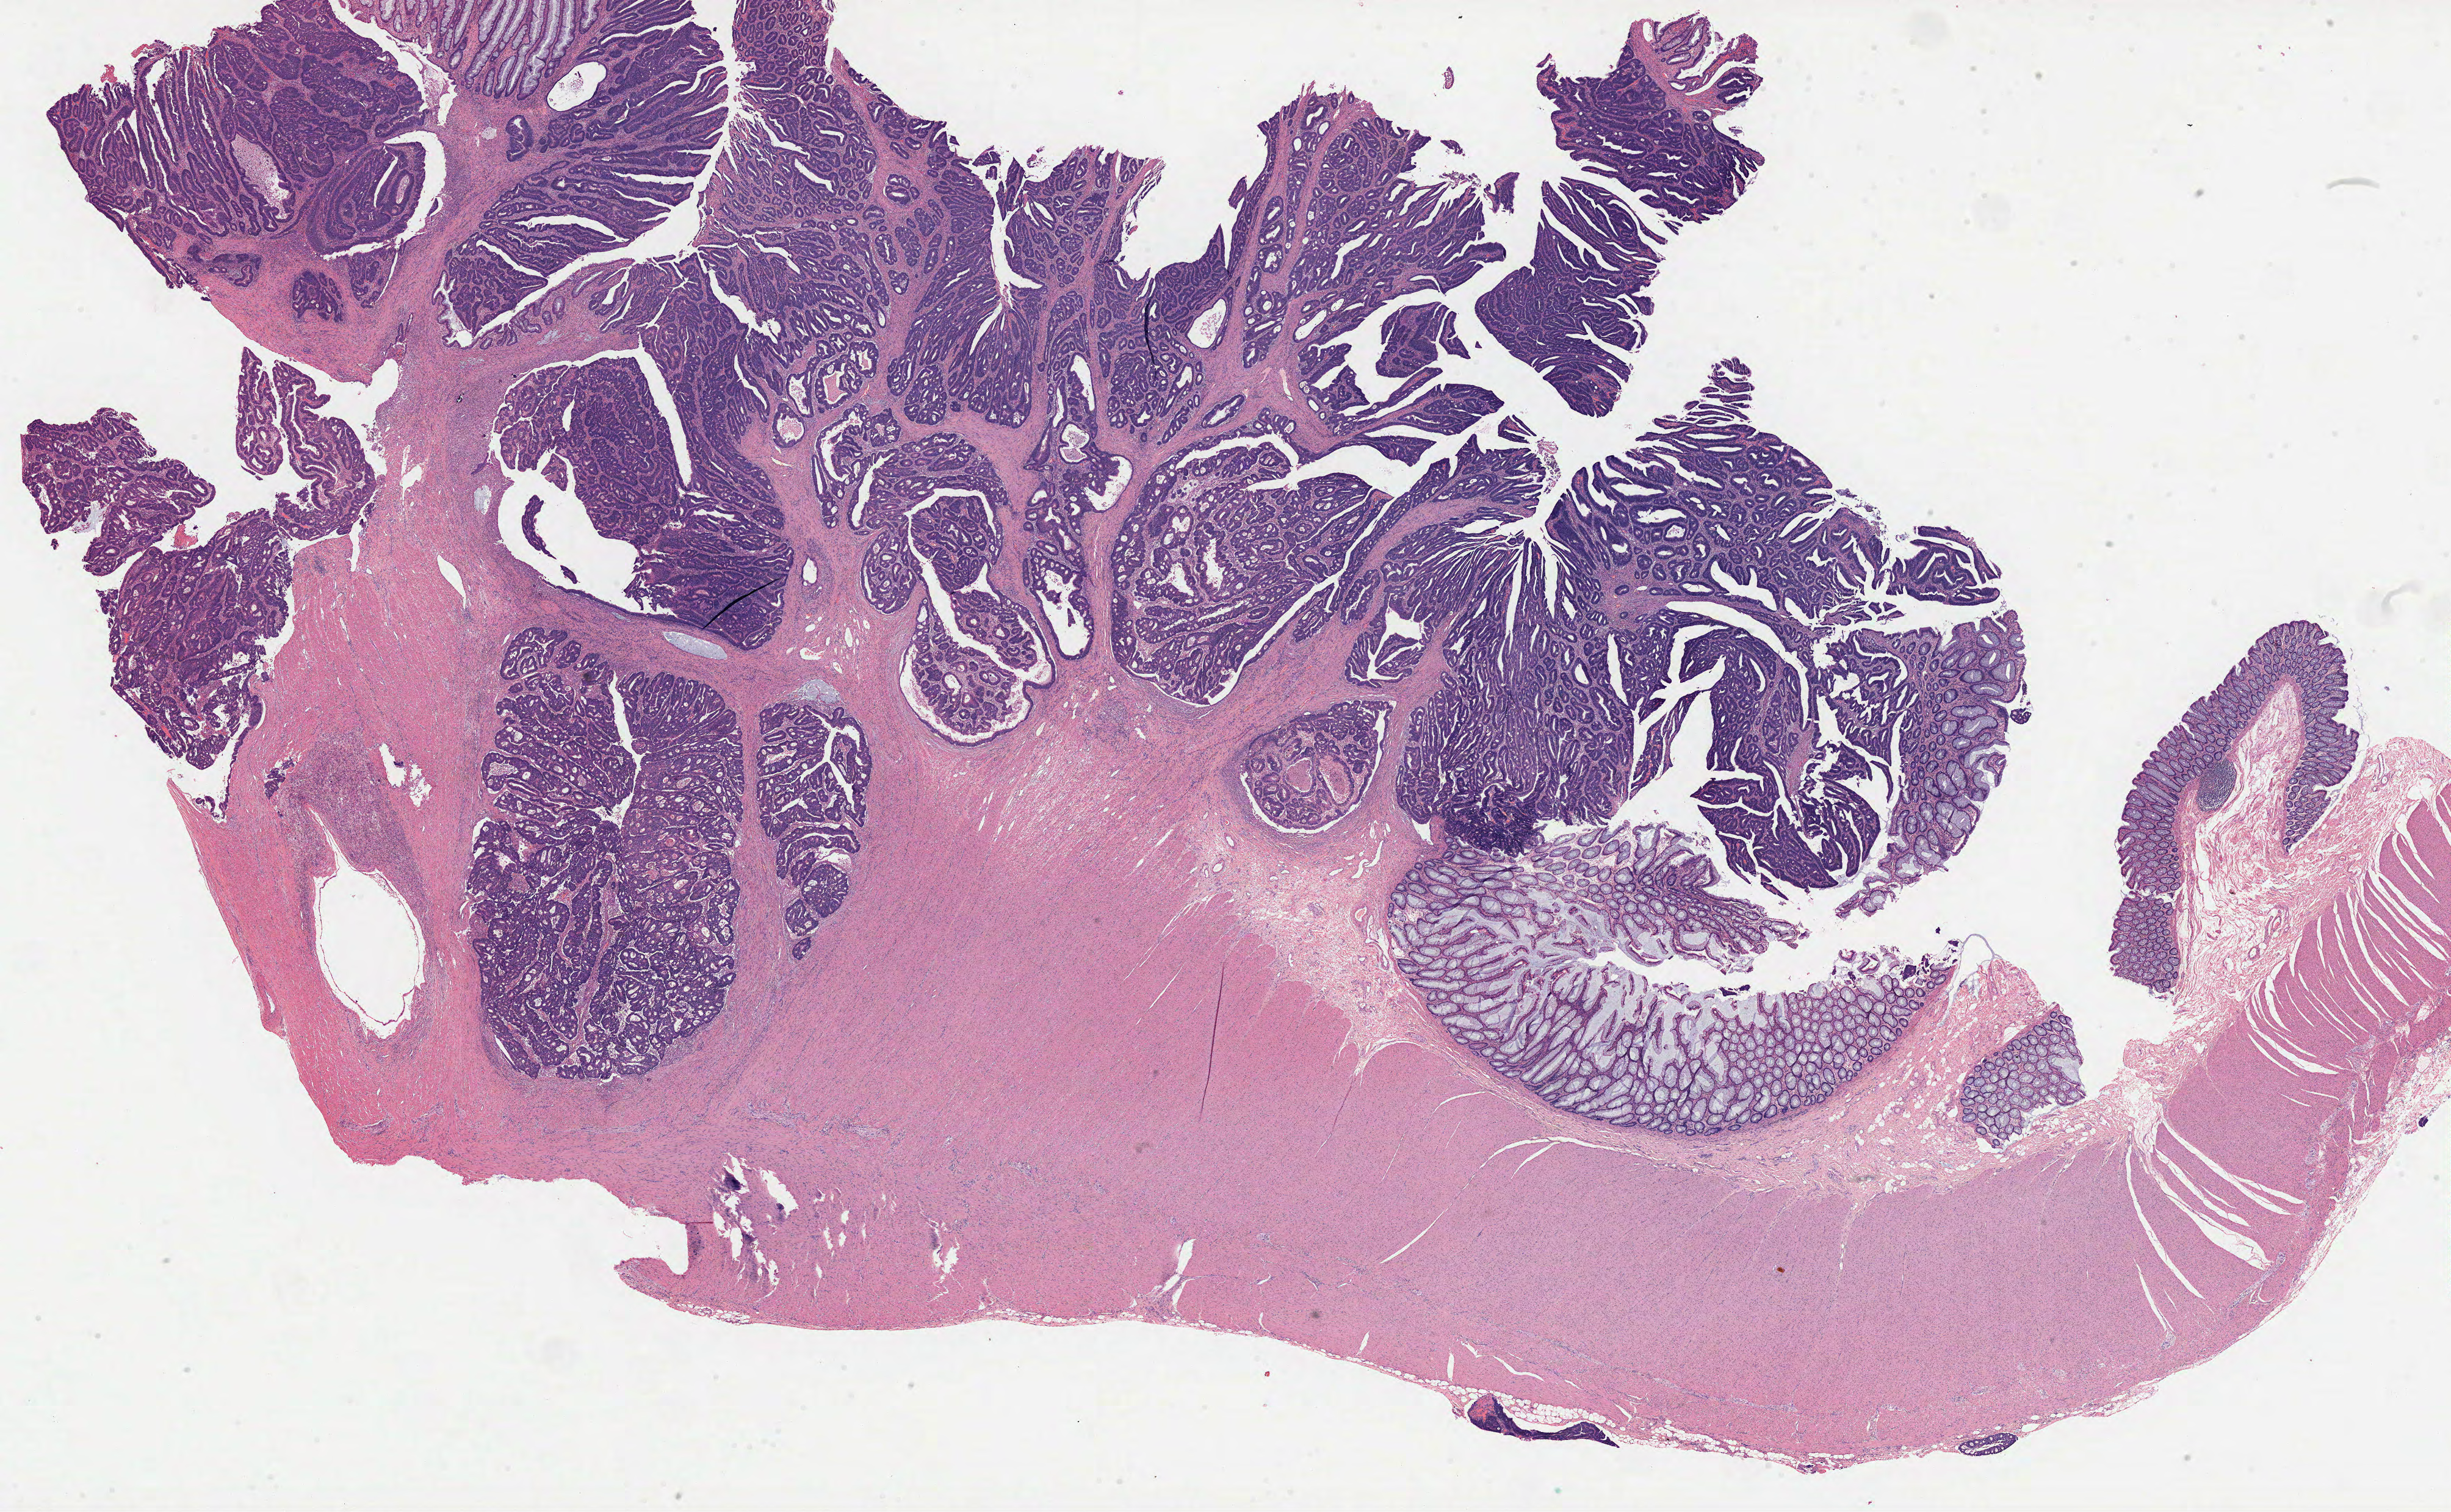
H&E-stained whole-slide image, shown as a low-resolution overview of the whole scanned area (about 32.4 x 20.0 mm, slide scanned at 40x). Formalin-fixed paraffin-embedded (FFPE) diagnostic section. Sample: primary tumour, colon. Patient: male, age at initial diagnosis 63 years.
* TNM: T2 N0 MX
* AJCC pathologic stage: I
* diagnosis: Adenocarcinoma, NOS (sigmoid colon)